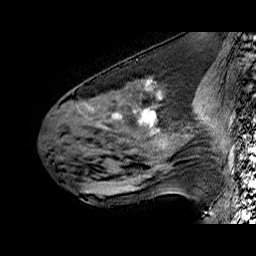
Breast MRI (dynamic contrast-enhanced), one sagittal slice; slice 26 of 60 in the series (ordered by position); dynamic contrast-enhanced series, time point 2 of 6 at this slice position (early post-contrast); 1.5 T; TE 6.4 ms, TR 32.9 ms; 4 mm slice thickness; 256 × 256 image matrix, field of view 200 × 200 mm. Female patient. Case-level facts recorded for this patient, not image findings: setting: breast cancer imaged before/during neoadjuvant chemotherapy; receptor status: HER2-positive.
Outlined on this slice (semi-automatic segmentation, software-assisted and operator-edited):
- analysis volume of interest (the breast-tissue region the enhancement analysis was run in; not a lesion): bounding box (x1, y1, x2, y2) in pixels: (51, 78, 196, 160)
- tumour enhancement mask (voxels above the 100 % enhancement threshold inside the analysis volume of interest): (87, 81, 160, 134)